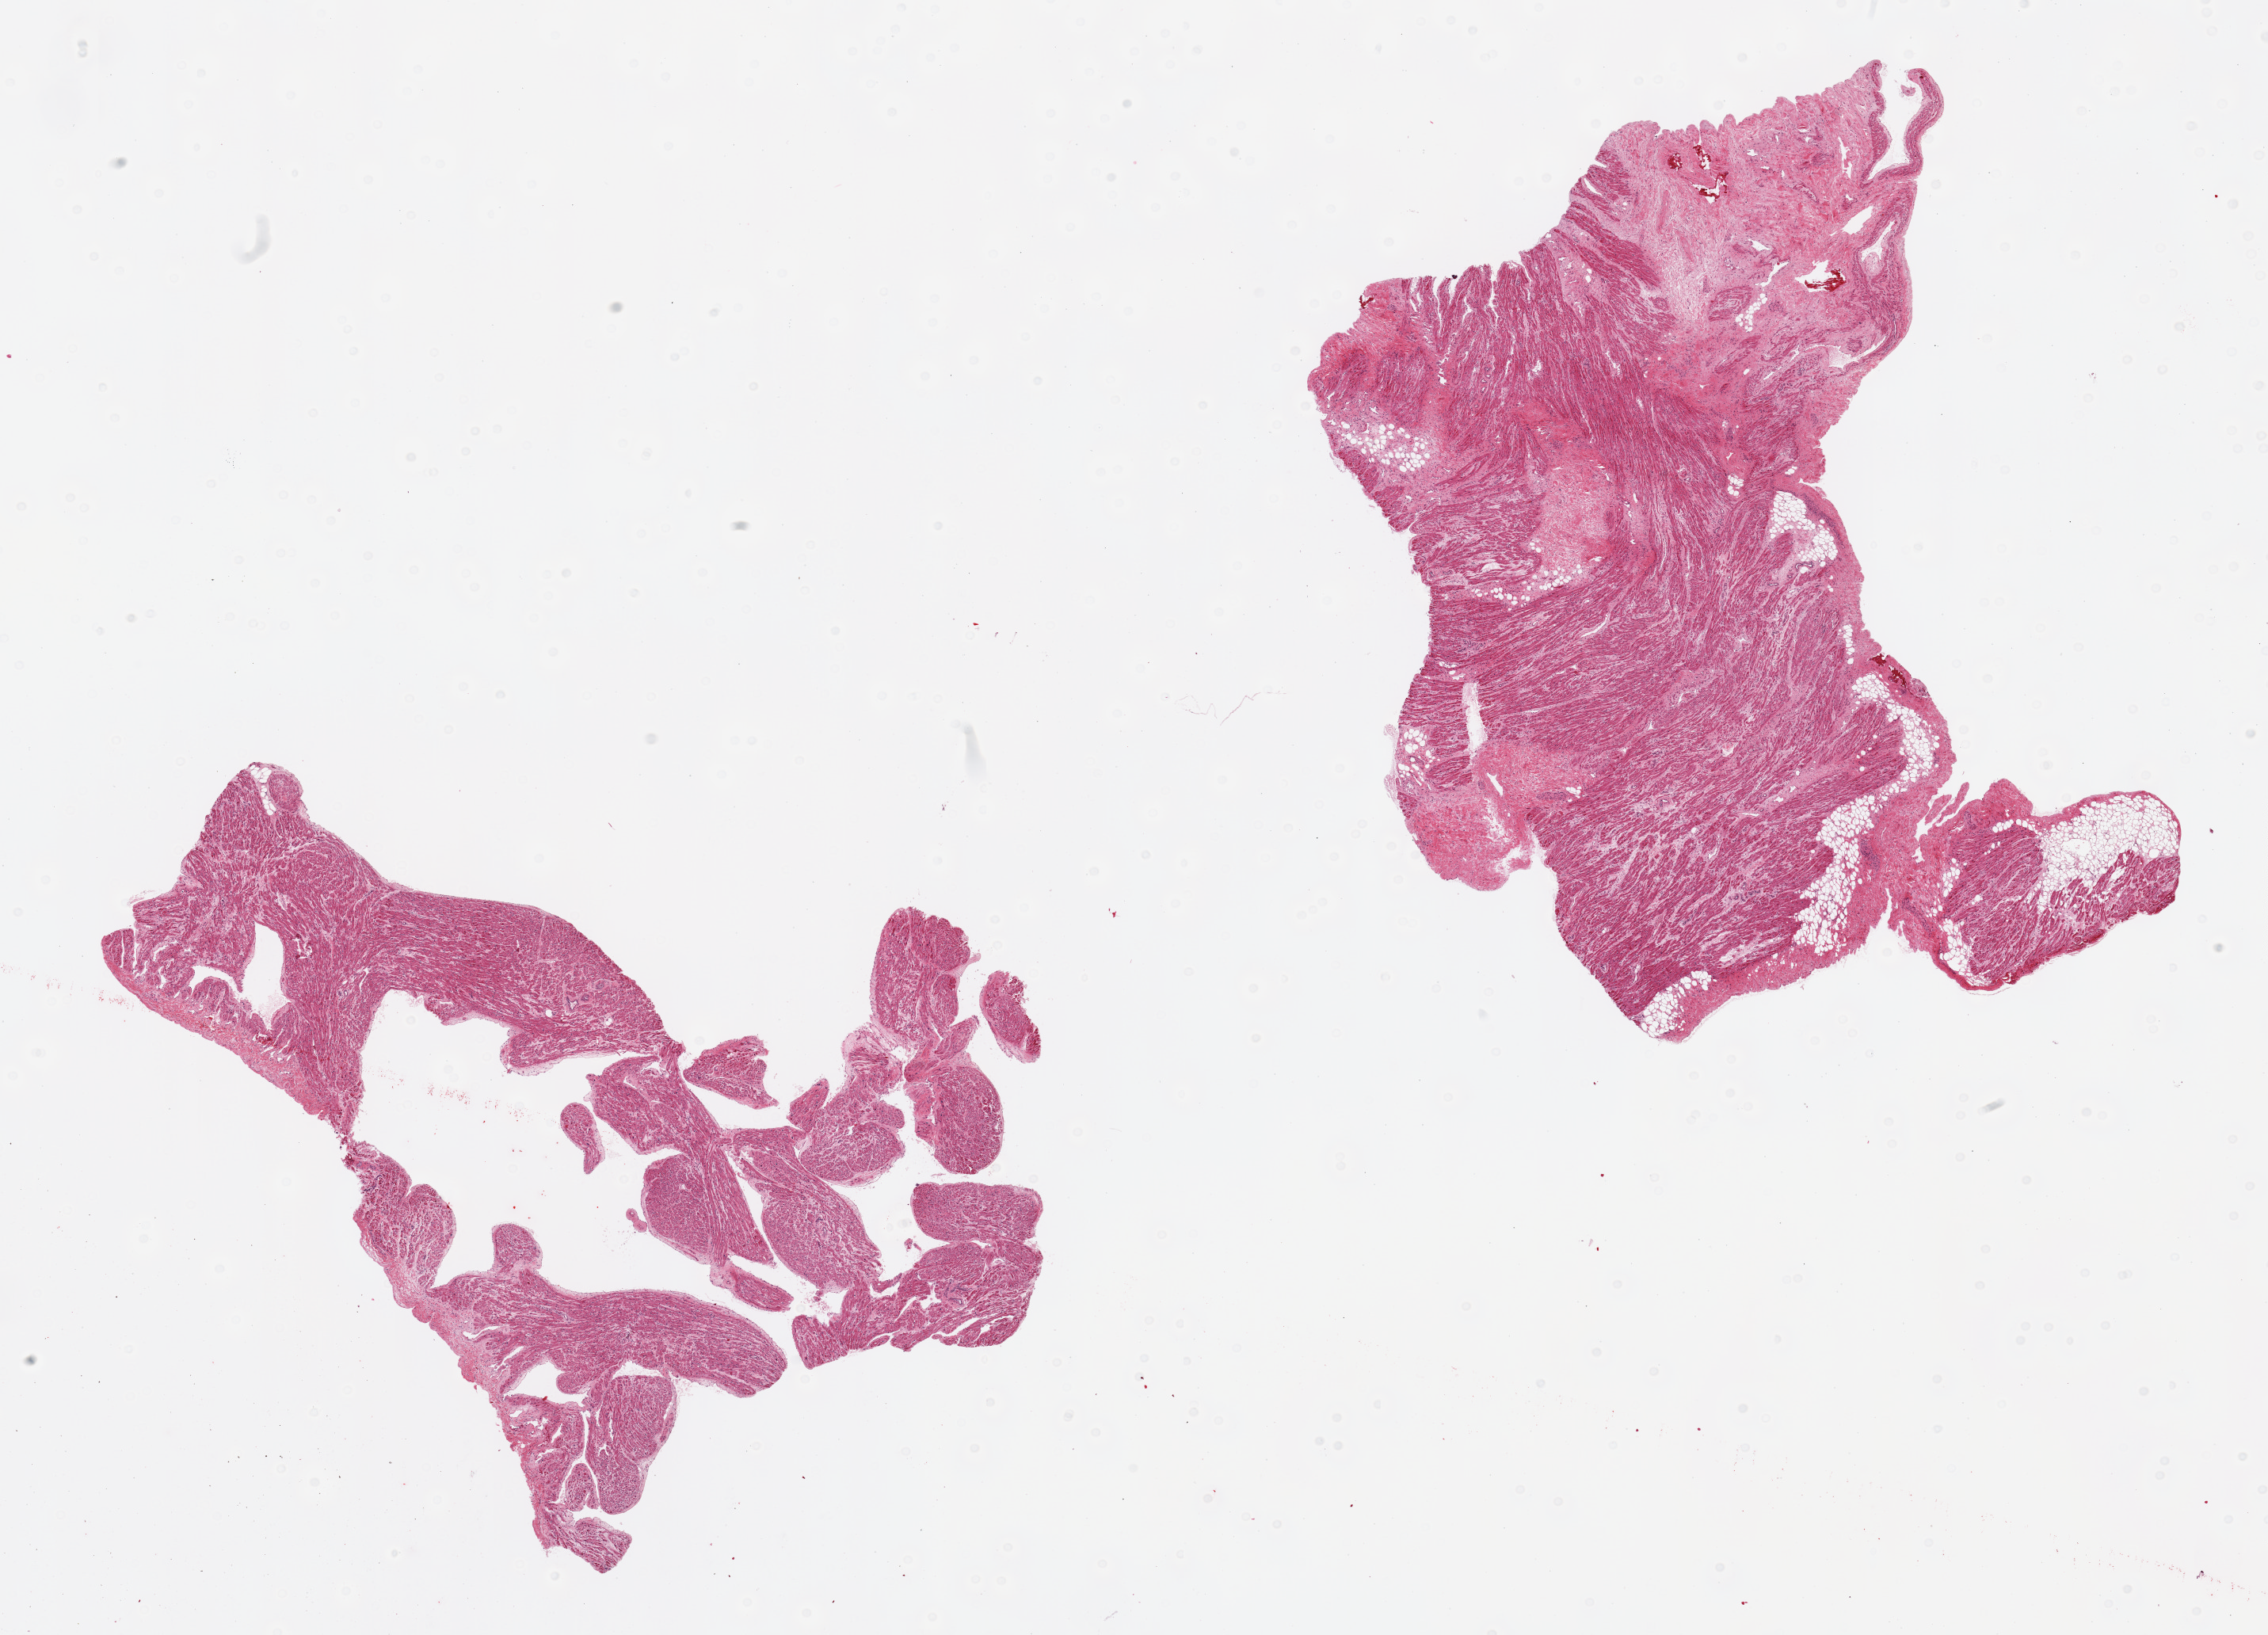
Whole-slide image, hematoxylin and eosin (H&E) stain, brightfield — low-resolution overview of the scanned area, about 22.6 x 16.3 mm (from a 20x scan). PAXgene-fixed paraffin-embedded (PFPE) section. Section of auricular appendage (target tissue). Tissue donor sample. Male donor.
Pathologist's review note for this sample: 2 pieces, one with 5-10% adipose tissue. Interstitial and larger patches of fibrosis.